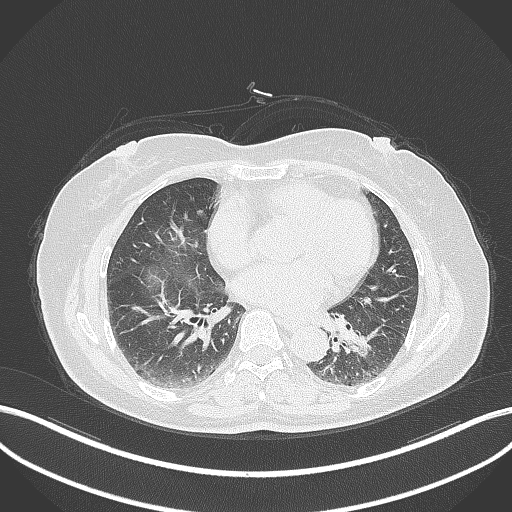
Chest CT, one axial slice. Position 163 of 311 along the scan axis. Reconstruction kernel B70f. Lung window (W 1500 / L -600 HU). 1 mm slice thickness. 512 × 512 image matrix. Female patient, age 59 years. From the clinical record (not read from this slice): clinical TNM (as recorded): T2a N0 M0; histopathological grade: G2-3.
Annotated regions visible in this slice (rectangle marked by the reading radiologist):
- lung tumour (recorded histology: adenocarcinoma): bounding box (x1, y1, x2, y2) in pixels: (337, 321, 383, 363)